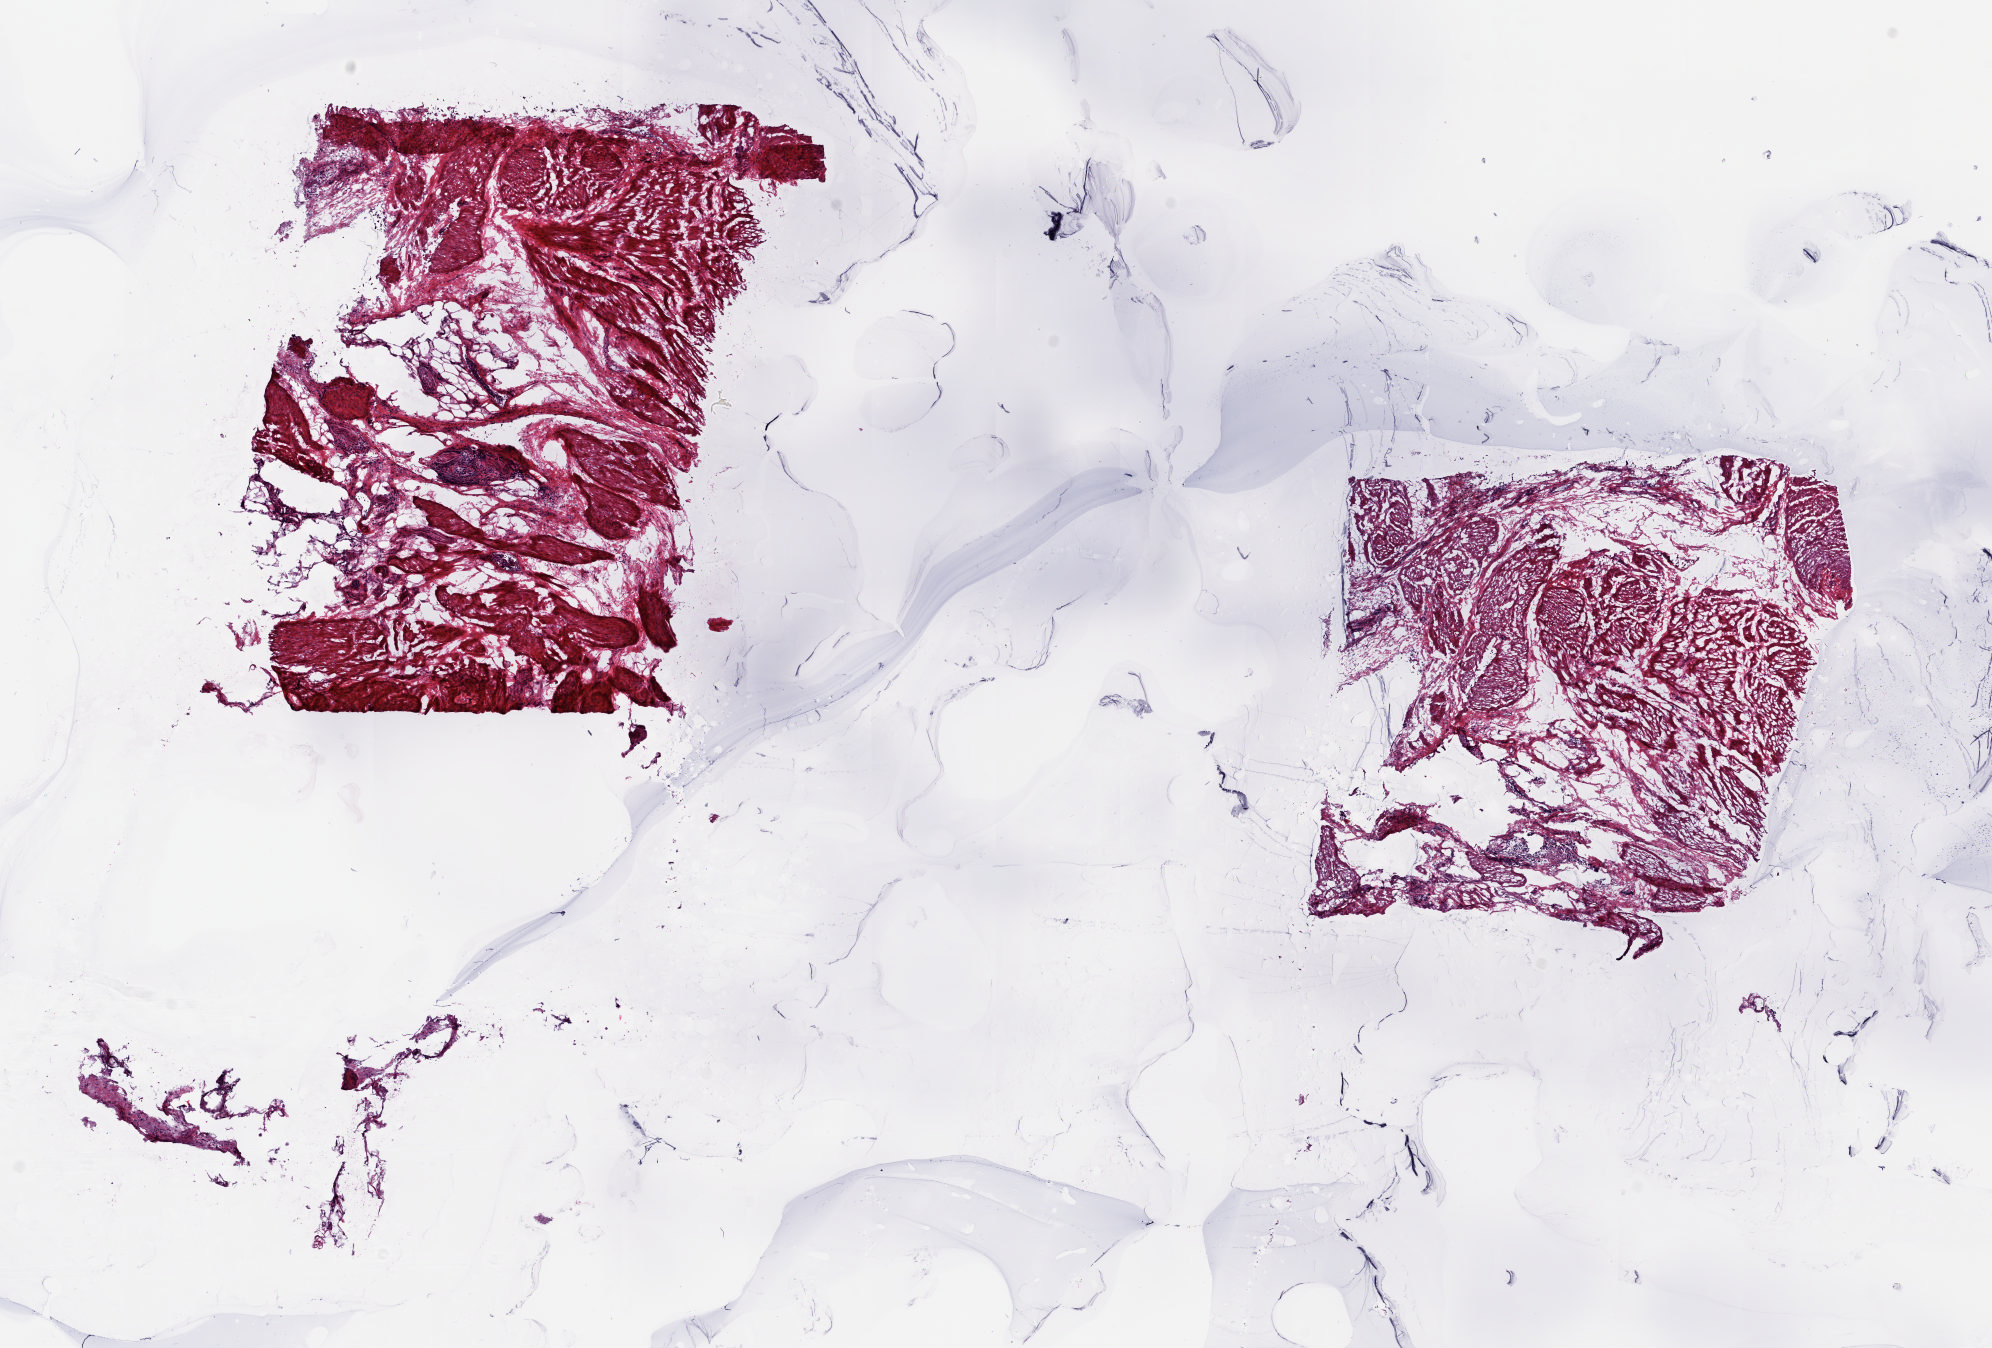
Hematoxylin and eosin (H&E) stained whole-slide image, low-resolution overview of the scanned area, about 15.8 x 10.7 mm (from a 20x scan). Frozen section. Bladder, solid tissue normal (non-tumour tissue) sample. Male patient; age at initial diagnosis 56 years. Composition of this section per pathologist review: tumour cells 0%, tumour nuclei 0%, normal cells 0%, stromal cells 100%, necrosis 0%. Infiltration values recorded for this section: lymphocyte infiltration 0%, monocyte infiltration 0%, neutrophil infiltration 0%.
This section: solid tissue normal (non-tumour) sample from the same patient. Patient diagnosis: Transitional cell carcinoma (dome of bladder).